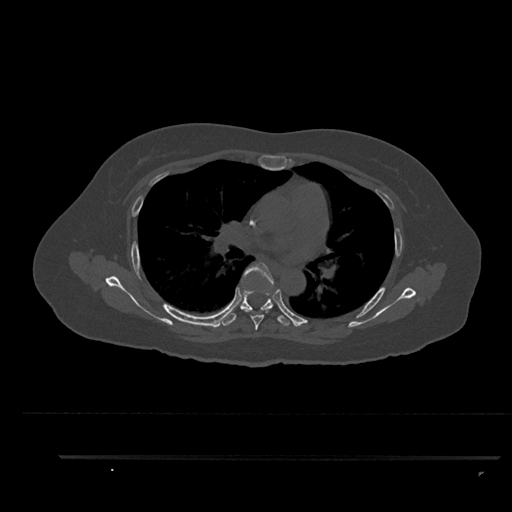
CT including the spine, one axial slice. Position 580 of 797 along the scan axis. Reconstruction kernel Br40s/3. Bone window (W 1800 / L 400 HU). 0.5 mm slice thickness. 512 × 512 image matrix. Patient: female, 44 years. Case-level facts recorded for this patient, not image findings: primary cancer: renal; vertebrae with lytic lesions (as recorded): L1.
Outlined on this slice (semi-automatic segmentation, software-assisted and operator-edited):
- T5 vertebra: bounding box [x1, y1, x2, y2] px = [242, 262, 274, 330]
- T6 vertebra: [222, 290, 290, 326]